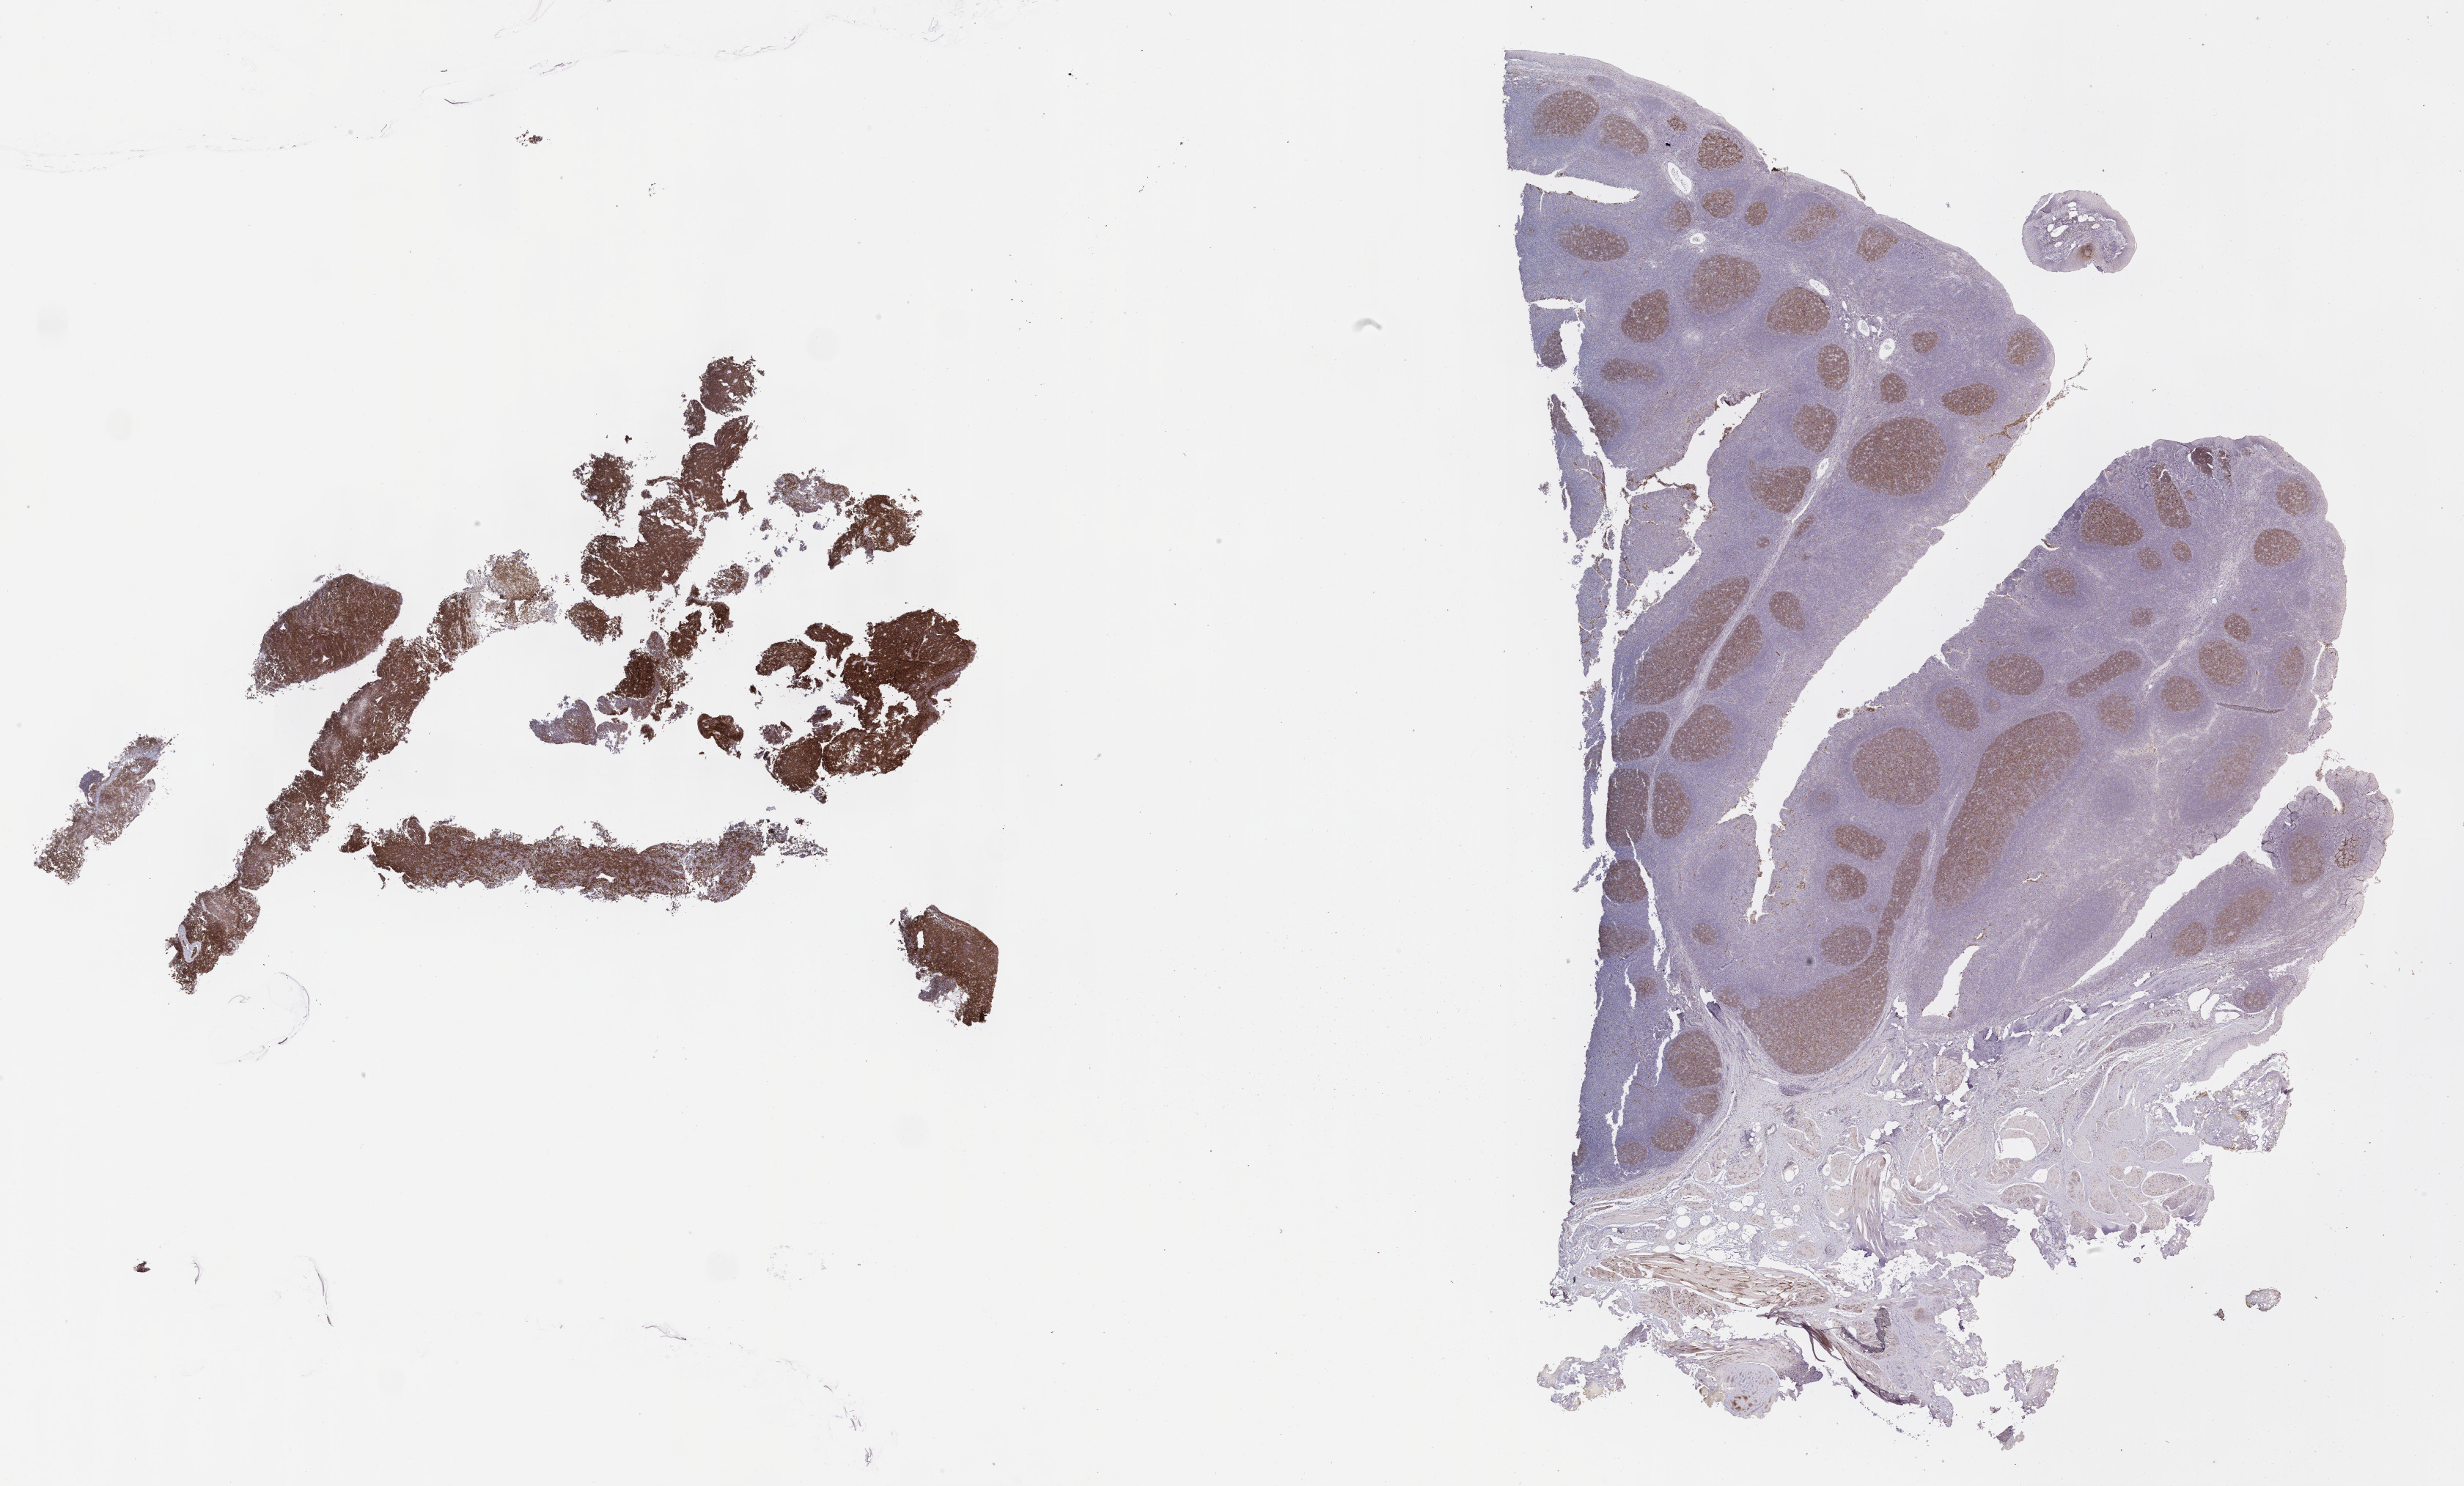
IHC for CD10, whole-slide image — a low-resolution overview of the entire scanned area, about 27.2 x 16.4 mm, specimen: tumor tissue, anatomic site: kidney. Male patient; age at initial diagnosis 3 years.
* histologic diagnosis: Burkitt lymphoma, NOS